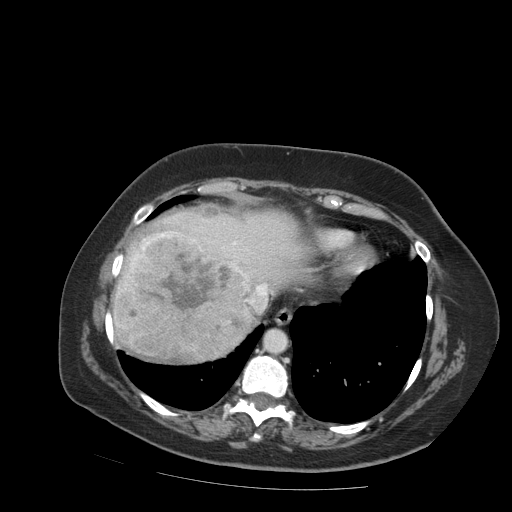
Contrast-enhanced abdominal CT (liver protocol), one axial slice. Position 75 of 99 along the scan axis. Soft-tissue window (W 400 / L 40 HU). 512 × 512 image matrix, field of view 400 × 400 mm. From the clinical record (not read from this slice): diagnosis: hepatocellular carcinoma (patient treated with transarterial chemoembolisation; whether this scan precedes or follows treatment is not stated here); TNM stage (as recorded): Stage-IVB.
Structures marked on this image (semi-automatically segmented with operator editing):
- liver parenchyma outside the tumour (the mass and vessels are separate outlines, so this box may not span the whole liver): box from (x=112, y=210) to (x=310, y=348) px
- mass: (x=111, y=231)–(x=262, y=365)
- liver vessels: (x=174, y=217)–(x=267, y=304)